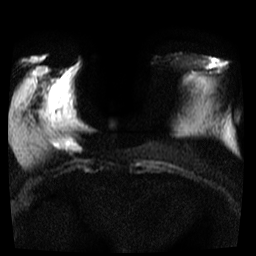
Breast MRI, one axial slice. Position 9 of 35 along the scan axis. Diffusion-weighted series; image 2 of 4 stored at this slice position (different b-values; order by instance number). 3 T. 256 × 256 image matrix, field of view 300 × 300 mm. Female patient.
Outlined on this slice (manually delineated by an expert):
- tumour on diffusion-weighted imaging: bounding box <59,139,82,153> (left, top, right, bottom; pixels)